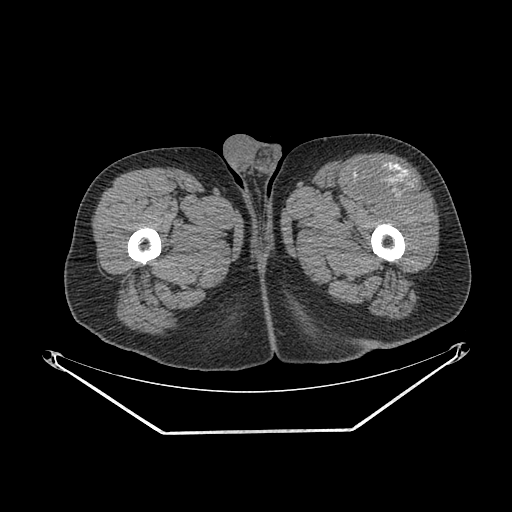
CT of an extremity soft-tissue mass (from a PET/CT study), one axial slice. Slice 254 of 267 in the series (ordered by position). 140 kVp. Soft-tissue window (W 400 / L 40 HU). 3.75 mm slice thickness. 512 × 512 image matrix, field of view 500 × 500 mm. Male patient. From the clinical record (not read from this slice): histological type: extraskeletal osteosarcoma; grade: high; site of the primary tumour: thigh.
Annotated regions visible in this slice (expert contour drawn on MRI and transferred to this co-registered scan by the dataset authors):
- gross tumour volume (mass): bounding box (x1, y1, x2, y2) in pixels: (363, 169, 419, 199)